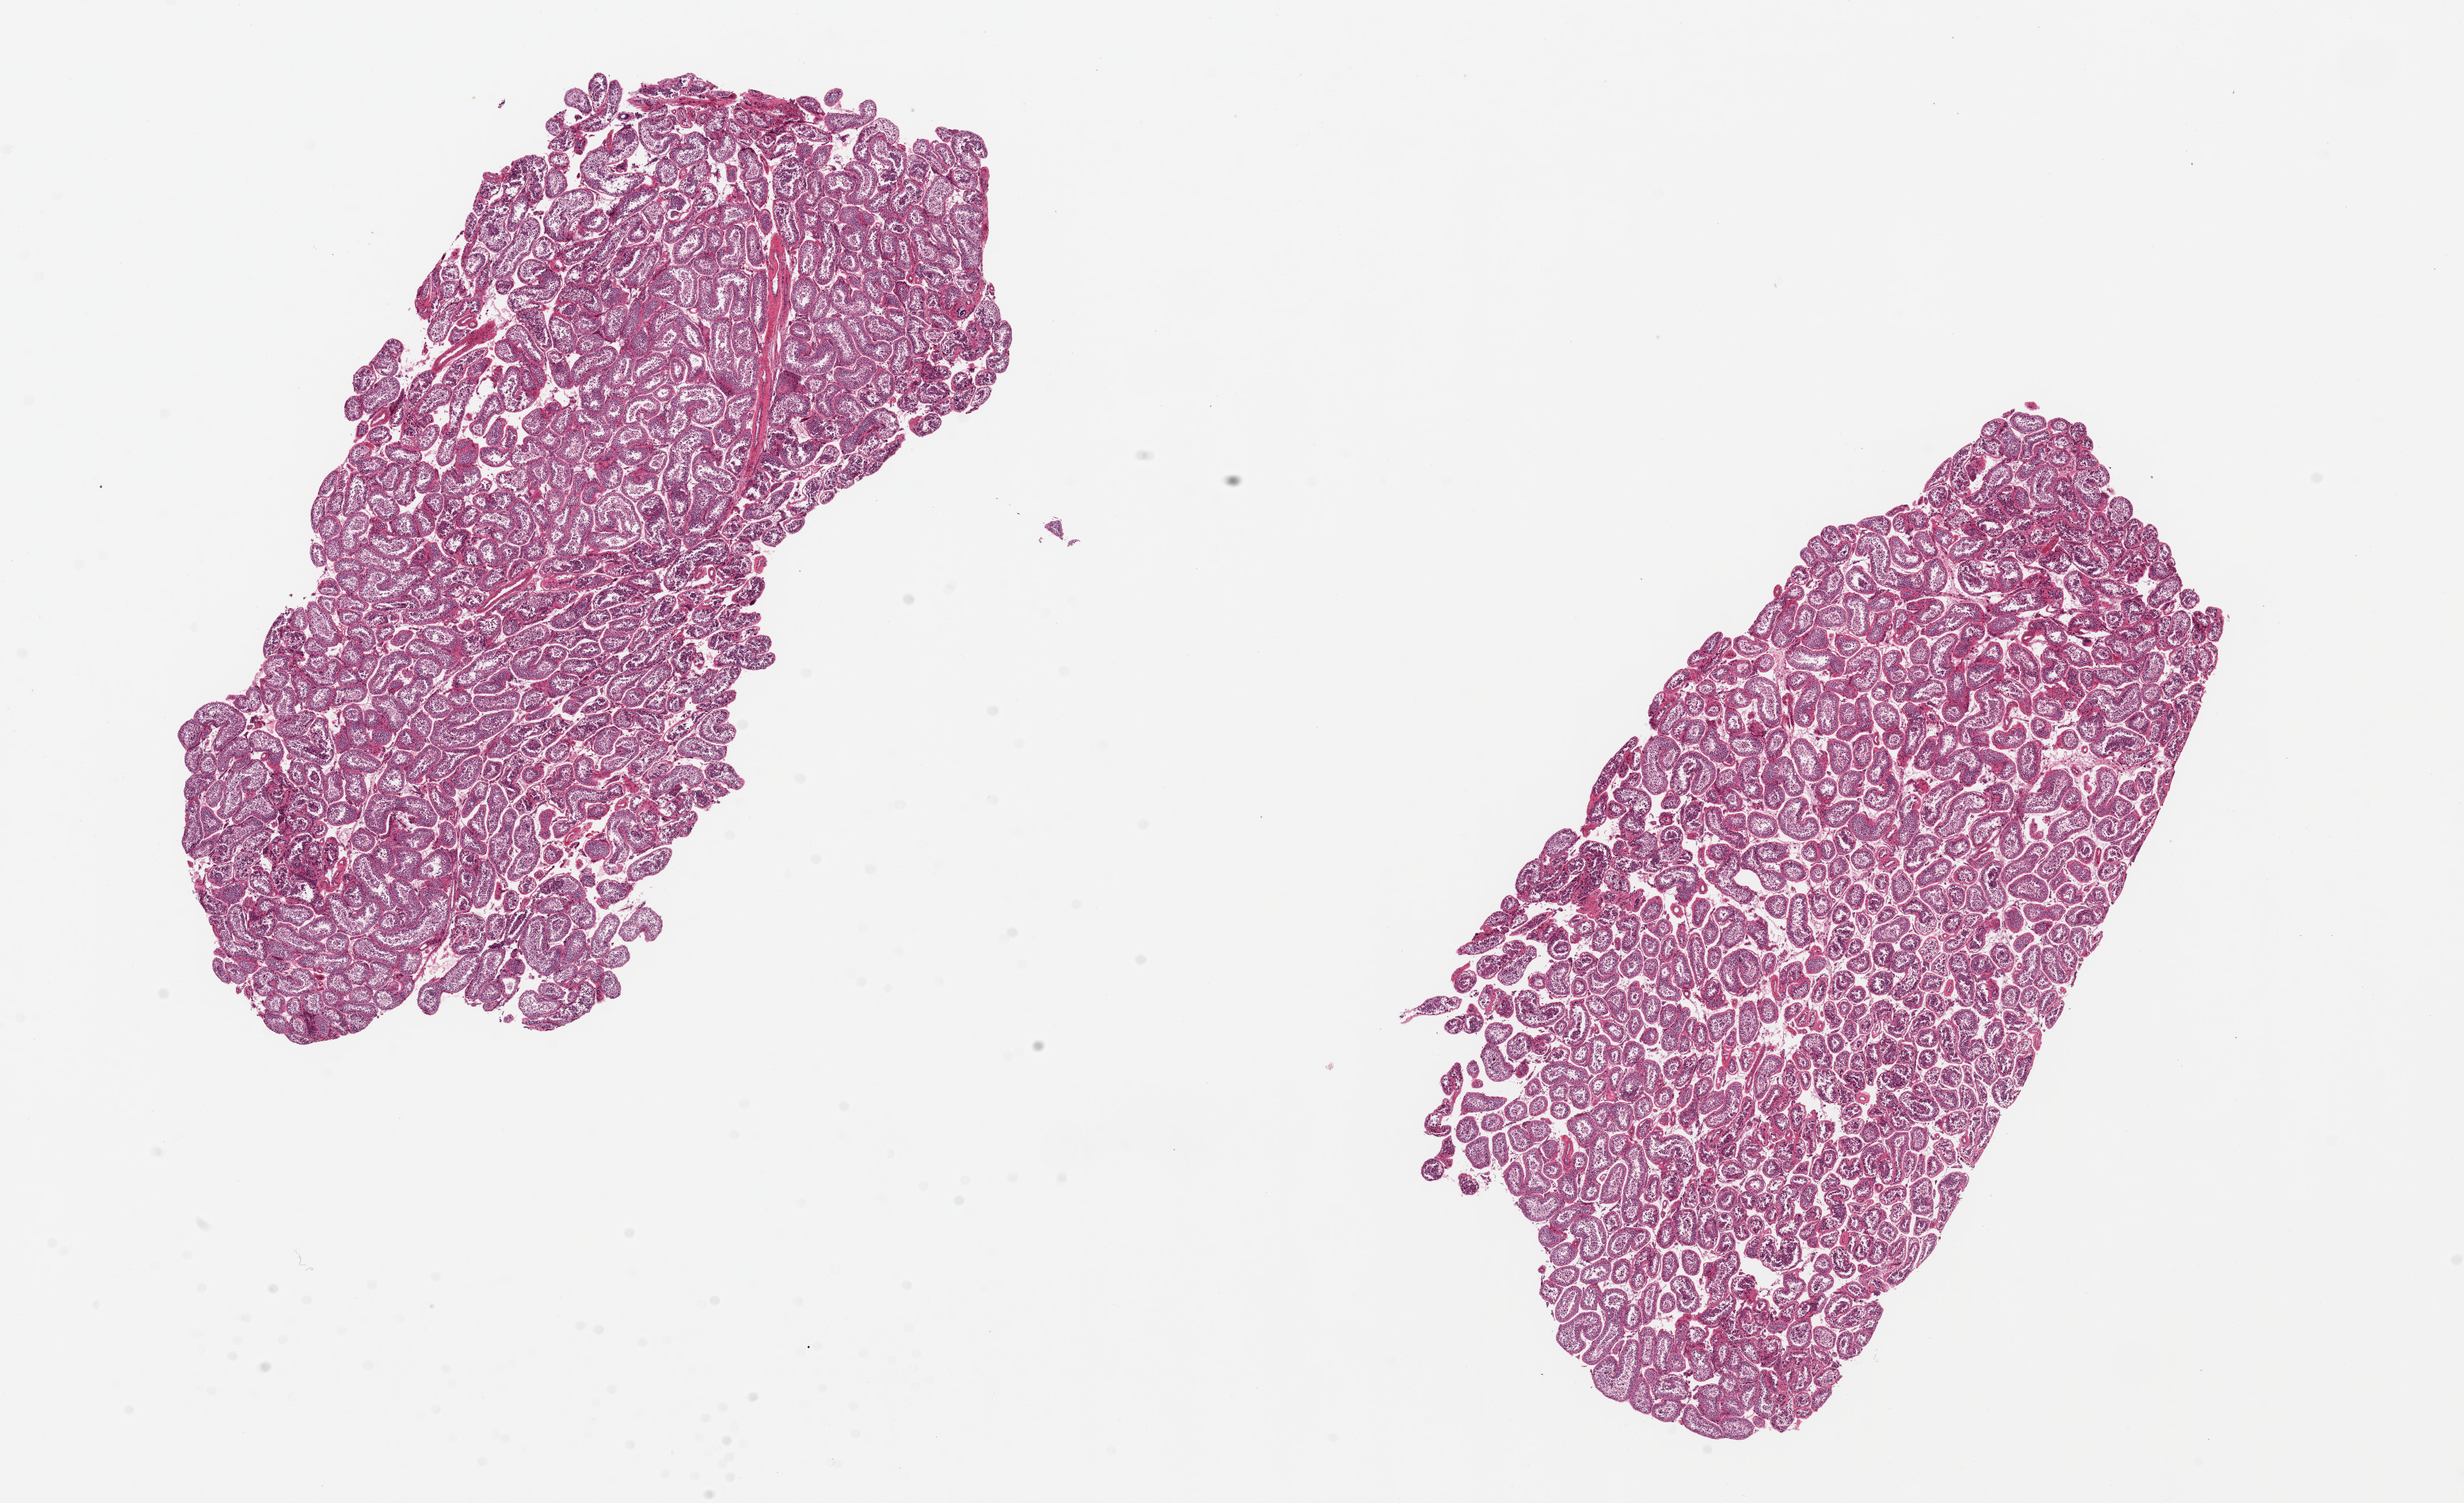
Whole-slide image, haematoxylin and eosin stain, brightfield — a low-resolution overview of the entire scanned area, about 24.6 x 15.0 mm (from a 20x scan); PAXgene-fixed paraffin-embedded (PFPE) section; section of testis (target tissue); tissue donor sample. Donor: male.
* pathologist's review note for this sample: 2 pieces, 11x5 & 10x6mm; spermatogenesis present